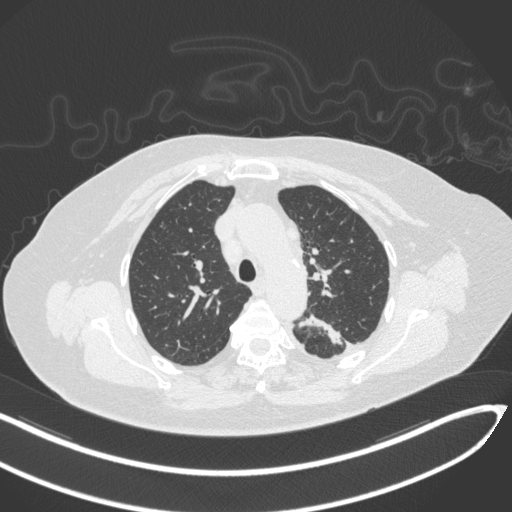
Chest CT, one axial slice. Position 228 of 270 along the scan axis. Reconstruction kernel B31f. 120 kVp. Lung window (W 1500 / L -600 HU). 1 mm slice thickness. 512 × 512 image matrix, field of view 400 × 400 mm. Female patient, age 76 years. Case-level facts recorded for this patient, not image findings: clinical TNM (as recorded): T1c N0 M0.
Annotated regions visible in this slice (bounding box drawn by a radiologist):
- lung tumour (recorded histology: adenocarcinoma): box from (x=295, y=311) to (x=346, y=348) px